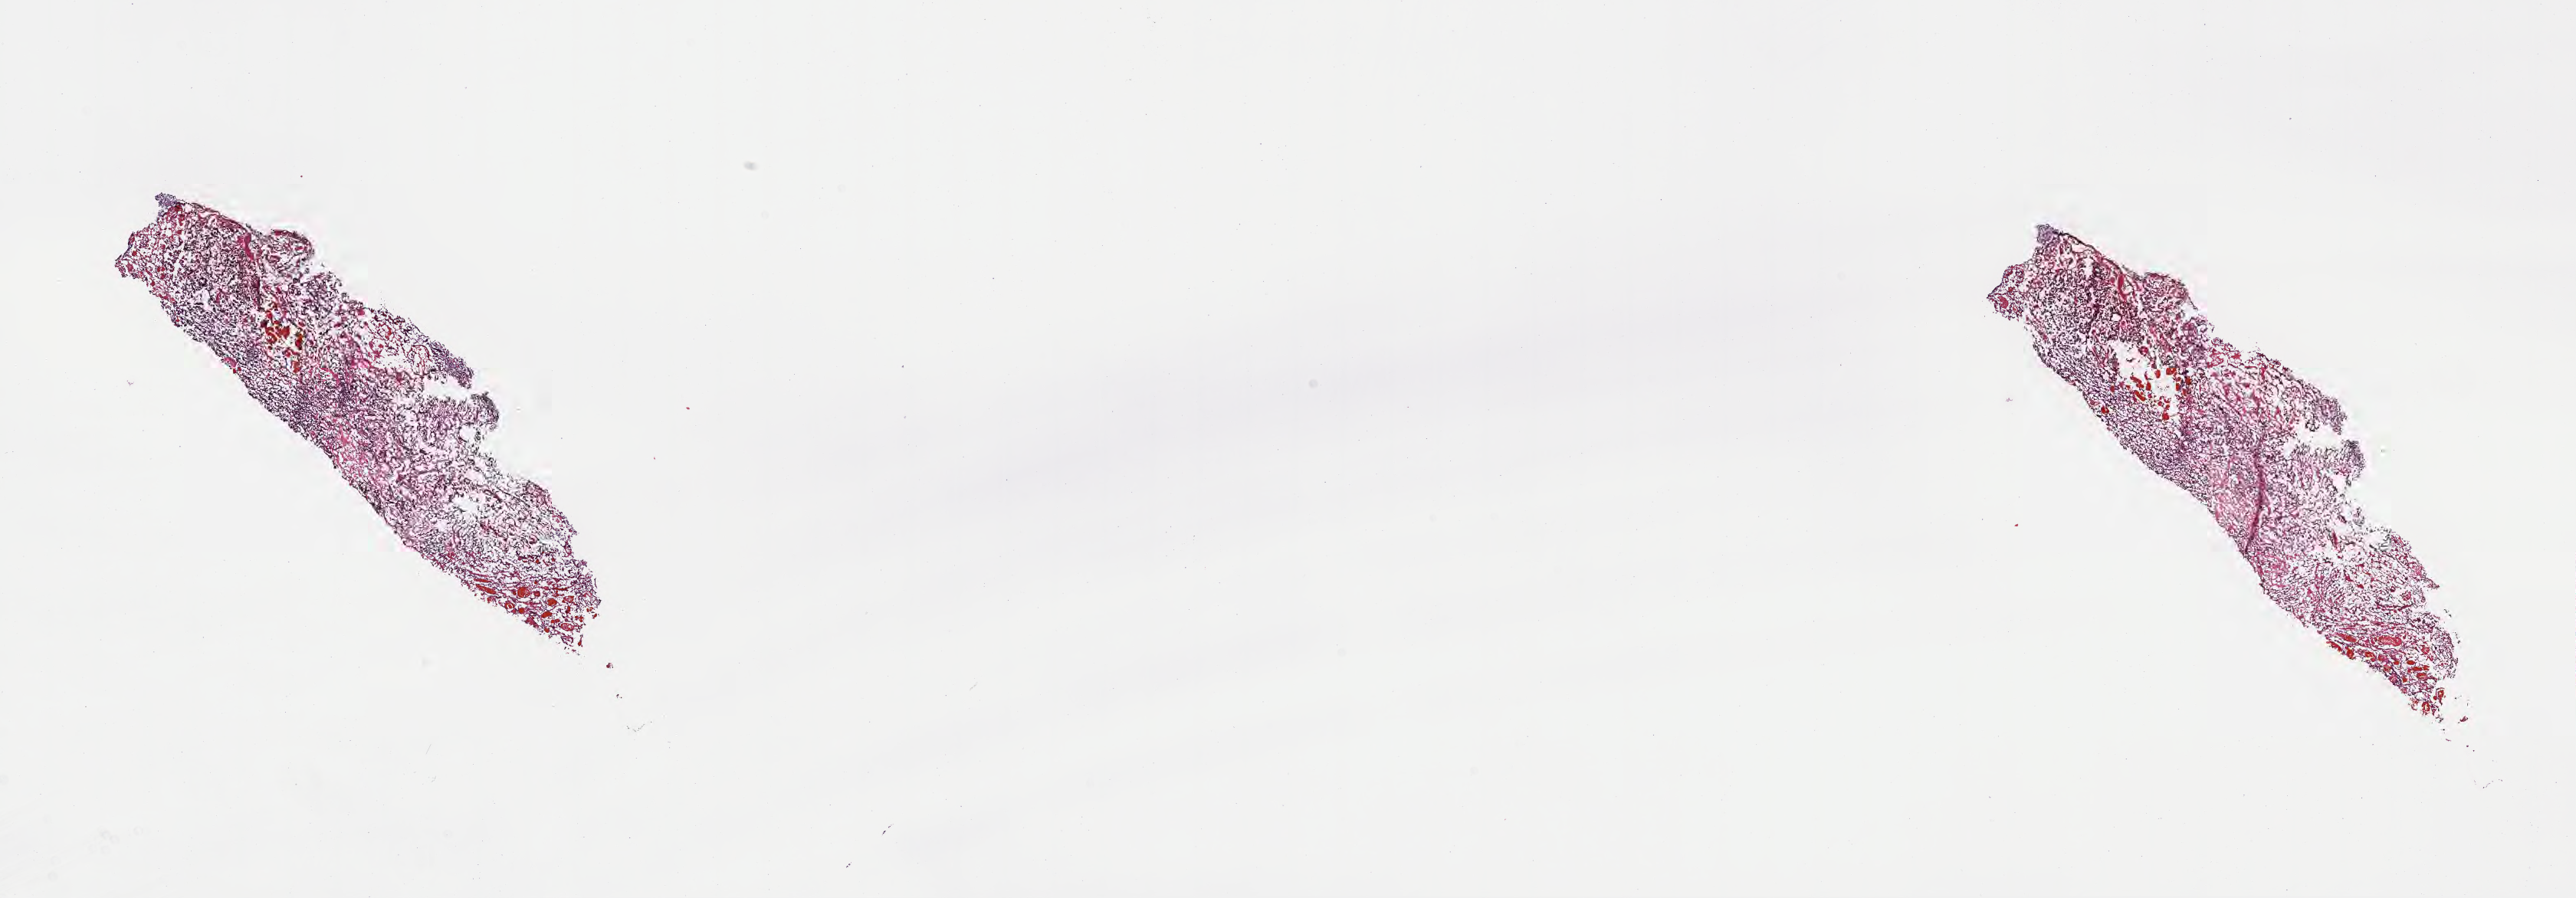
Whole-slide image, hematoxylin and eosin (H&E) stain of tumor tissue from the brain — a low-resolution overview of the entire scanned area, about 27.2 x 9.5 mm; cryosection (OCT / tissue freezing medium). Patient: female, age 119 months (9 years 11 months).
Recorded diagnosis: Medulloblastoma, NOS.